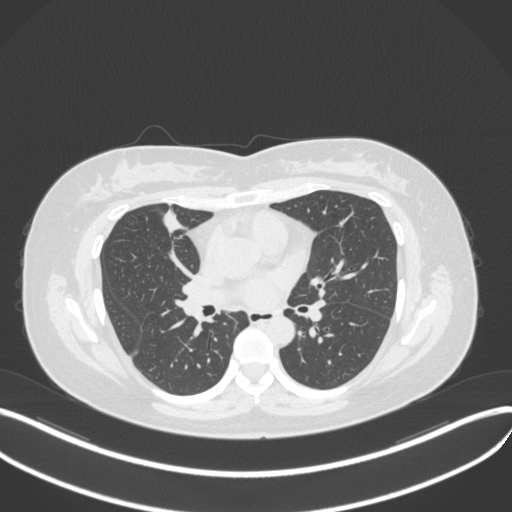
Chest CT, one axial slice; slice 166 of 272 in the series (ordered by position); reconstruction kernel B31f; lung window (W 1500 / L -600 HU); 512 × 512 image matrix, field of view 400 × 400 mm. Female patient, age 42 years. From the clinical record (not read from this slice): clinical TNM (as recorded): T1b N0 M0.
Structures marked on this image (rectangle marked by the reading radiologist):
- lung tumour (recorded histology: adenocarcinoma): bounding box (x1, y1, x2, y2) in pixels: (160, 206, 192, 240)